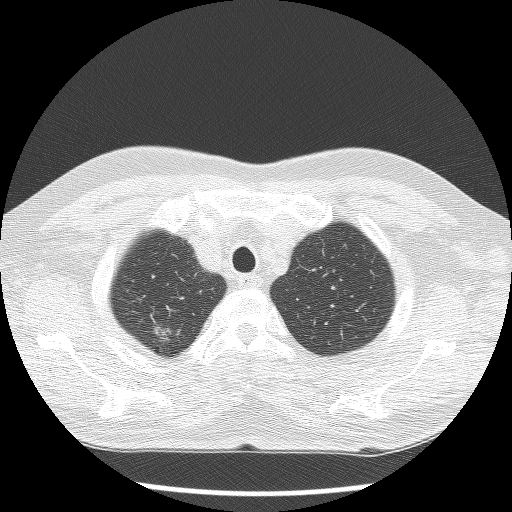
Axial slice from a low-dose chest CT screening exam; baseline annual screen; lung window (W 1500 / L -600 HU); 120 kVp. Male, age 70 years at enrolment. Current smoker at enrolment.
Expert-annotated lung lesion, bounding box (x1, y1, x2, y2) in pixels: (139, 316, 182, 353). Screening reader's record for this exam (one nodule recorded; not confirmed to be the boxed lesion): non-calcified nodule or mass ≥4 mm, right upper lobe, 12 × 10 mm, smooth margins, soft tissue attenuation. Later outcome: lung cancer diagnosed 14 days after this screen — large cell neuroendocrine carcinoma, right upper lobe, poorly differentiated (G3), stage IA (AJCC 6th edition), 15 mm at pathology.